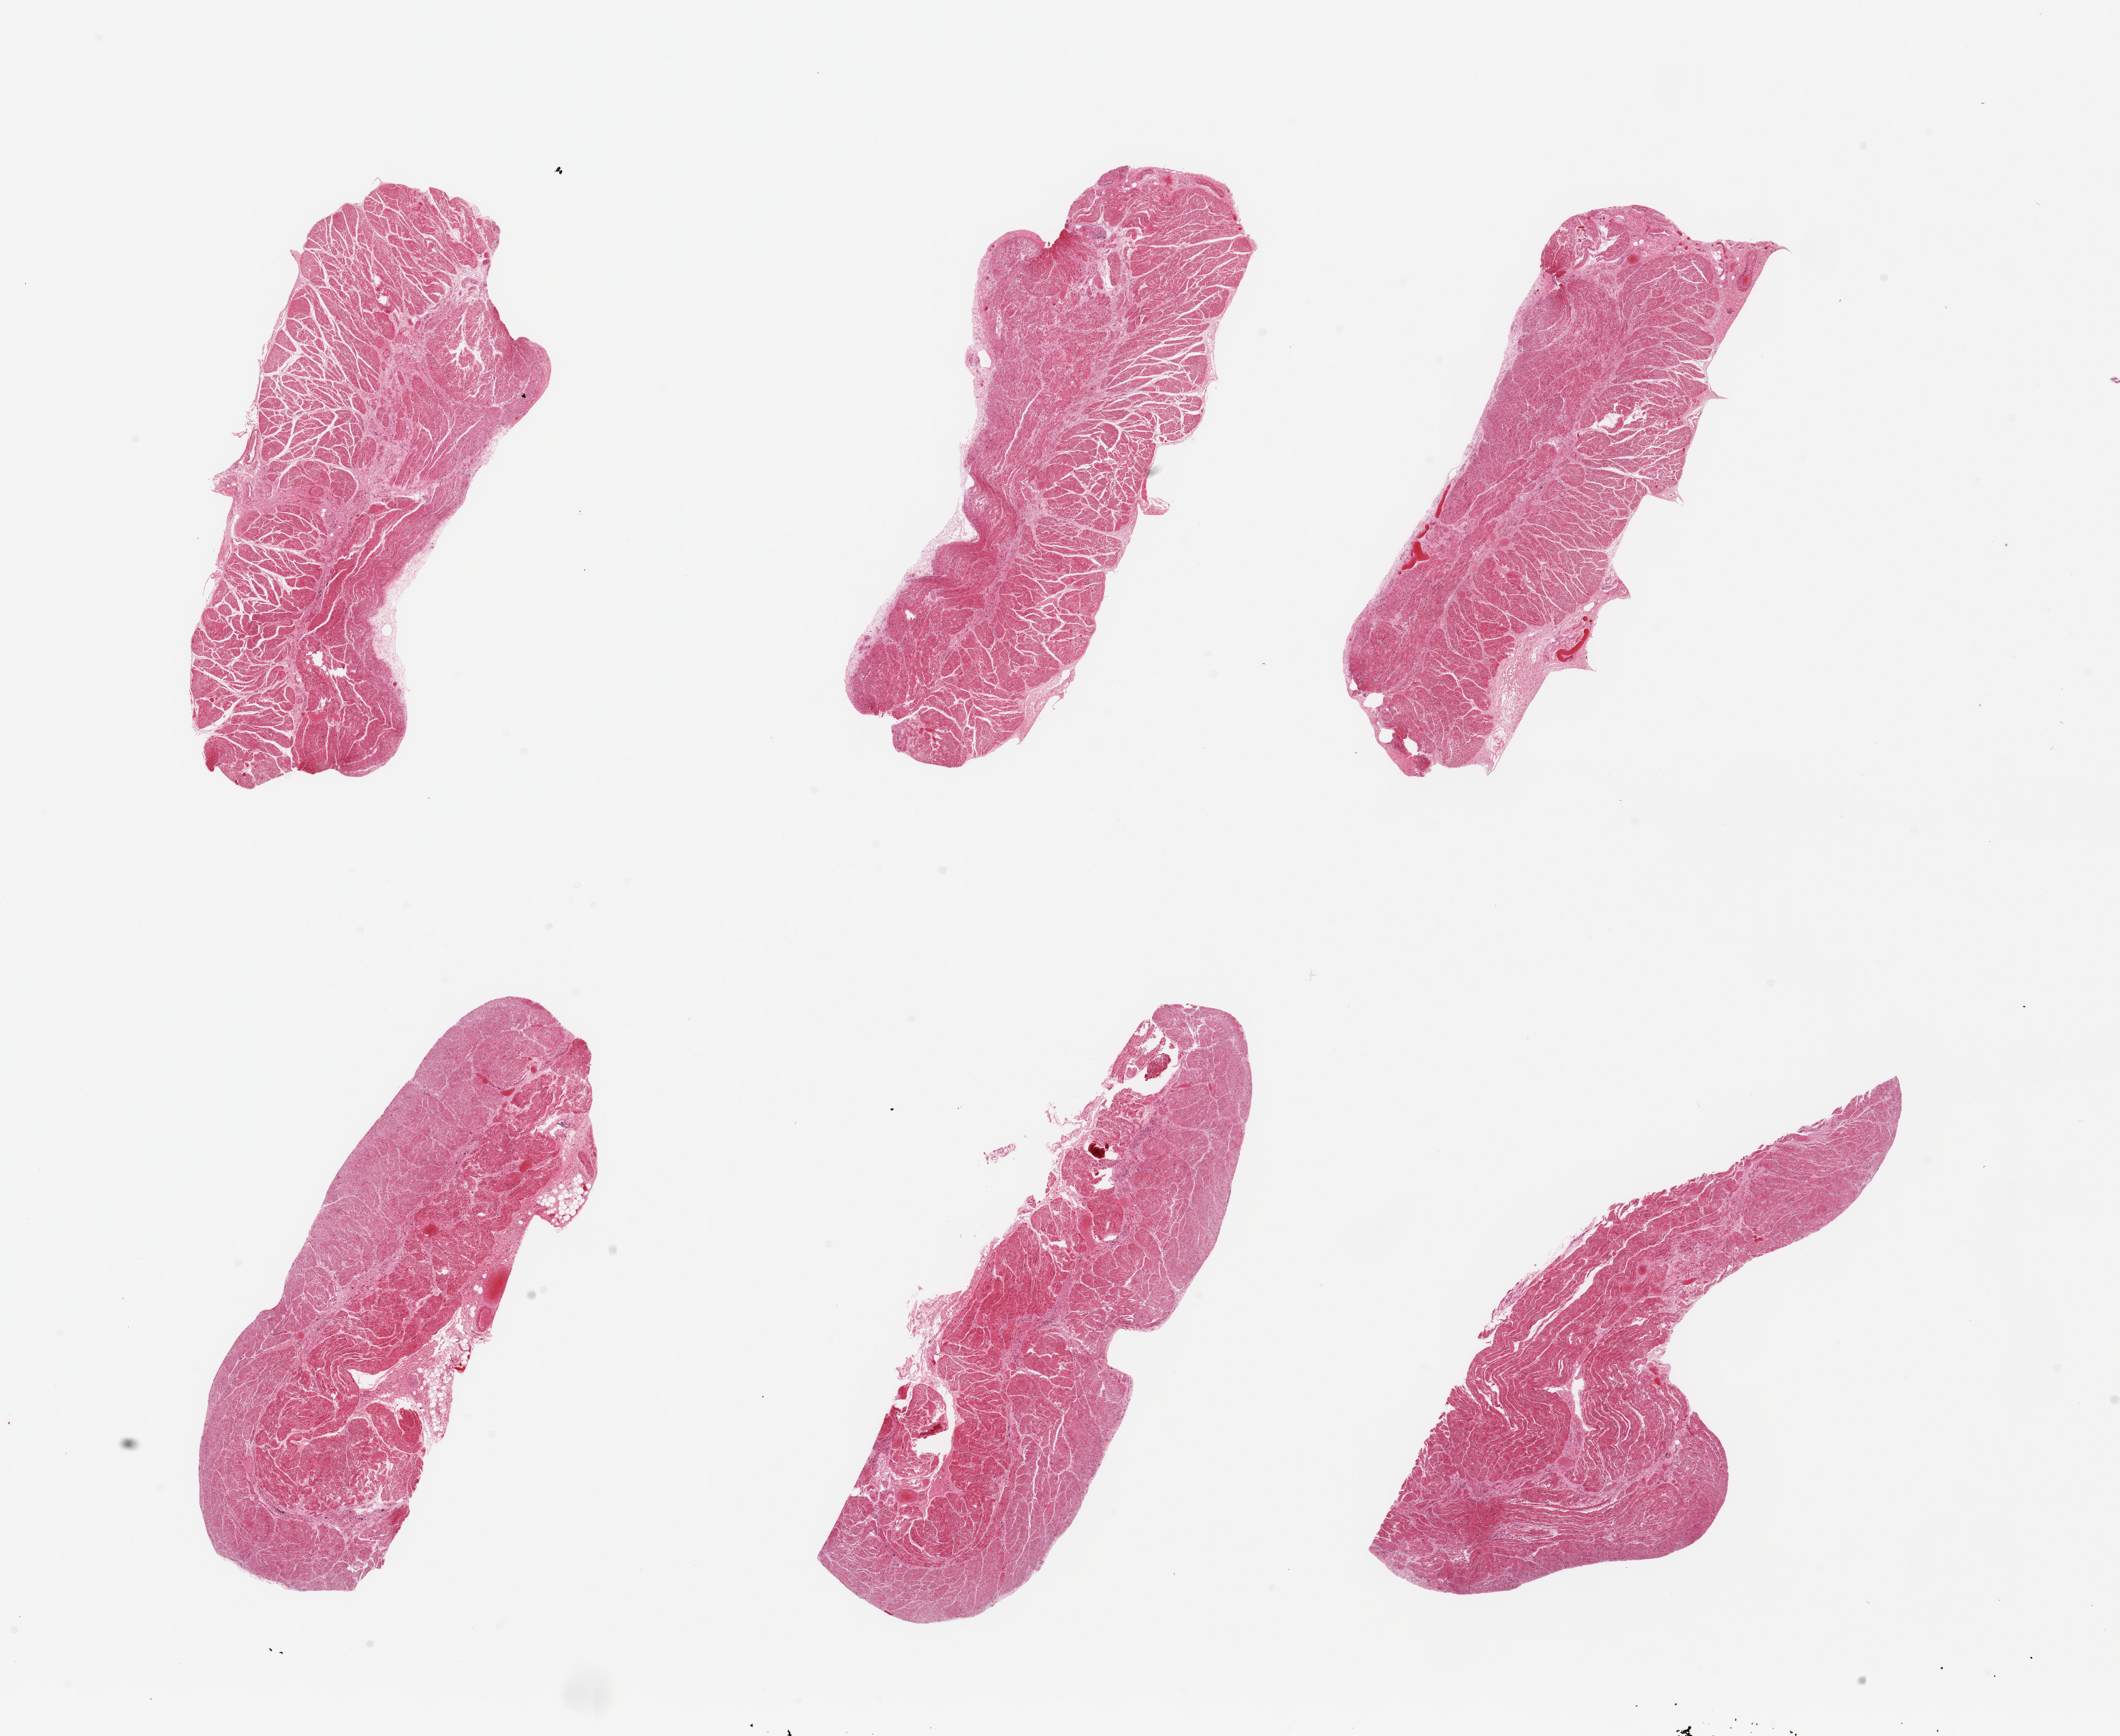
Whole-slide image, H&E stain, shown as a low-resolution overview of the whole scanned area (about 24.6 x 20.2 mm), PAXgene-fixed, paraffin-embedded tissue, section of esophageal muscle (target tissue), tissue donor sample.
• reviewer comment on this tissue sample: 6 pieces, confirmed target muscularis